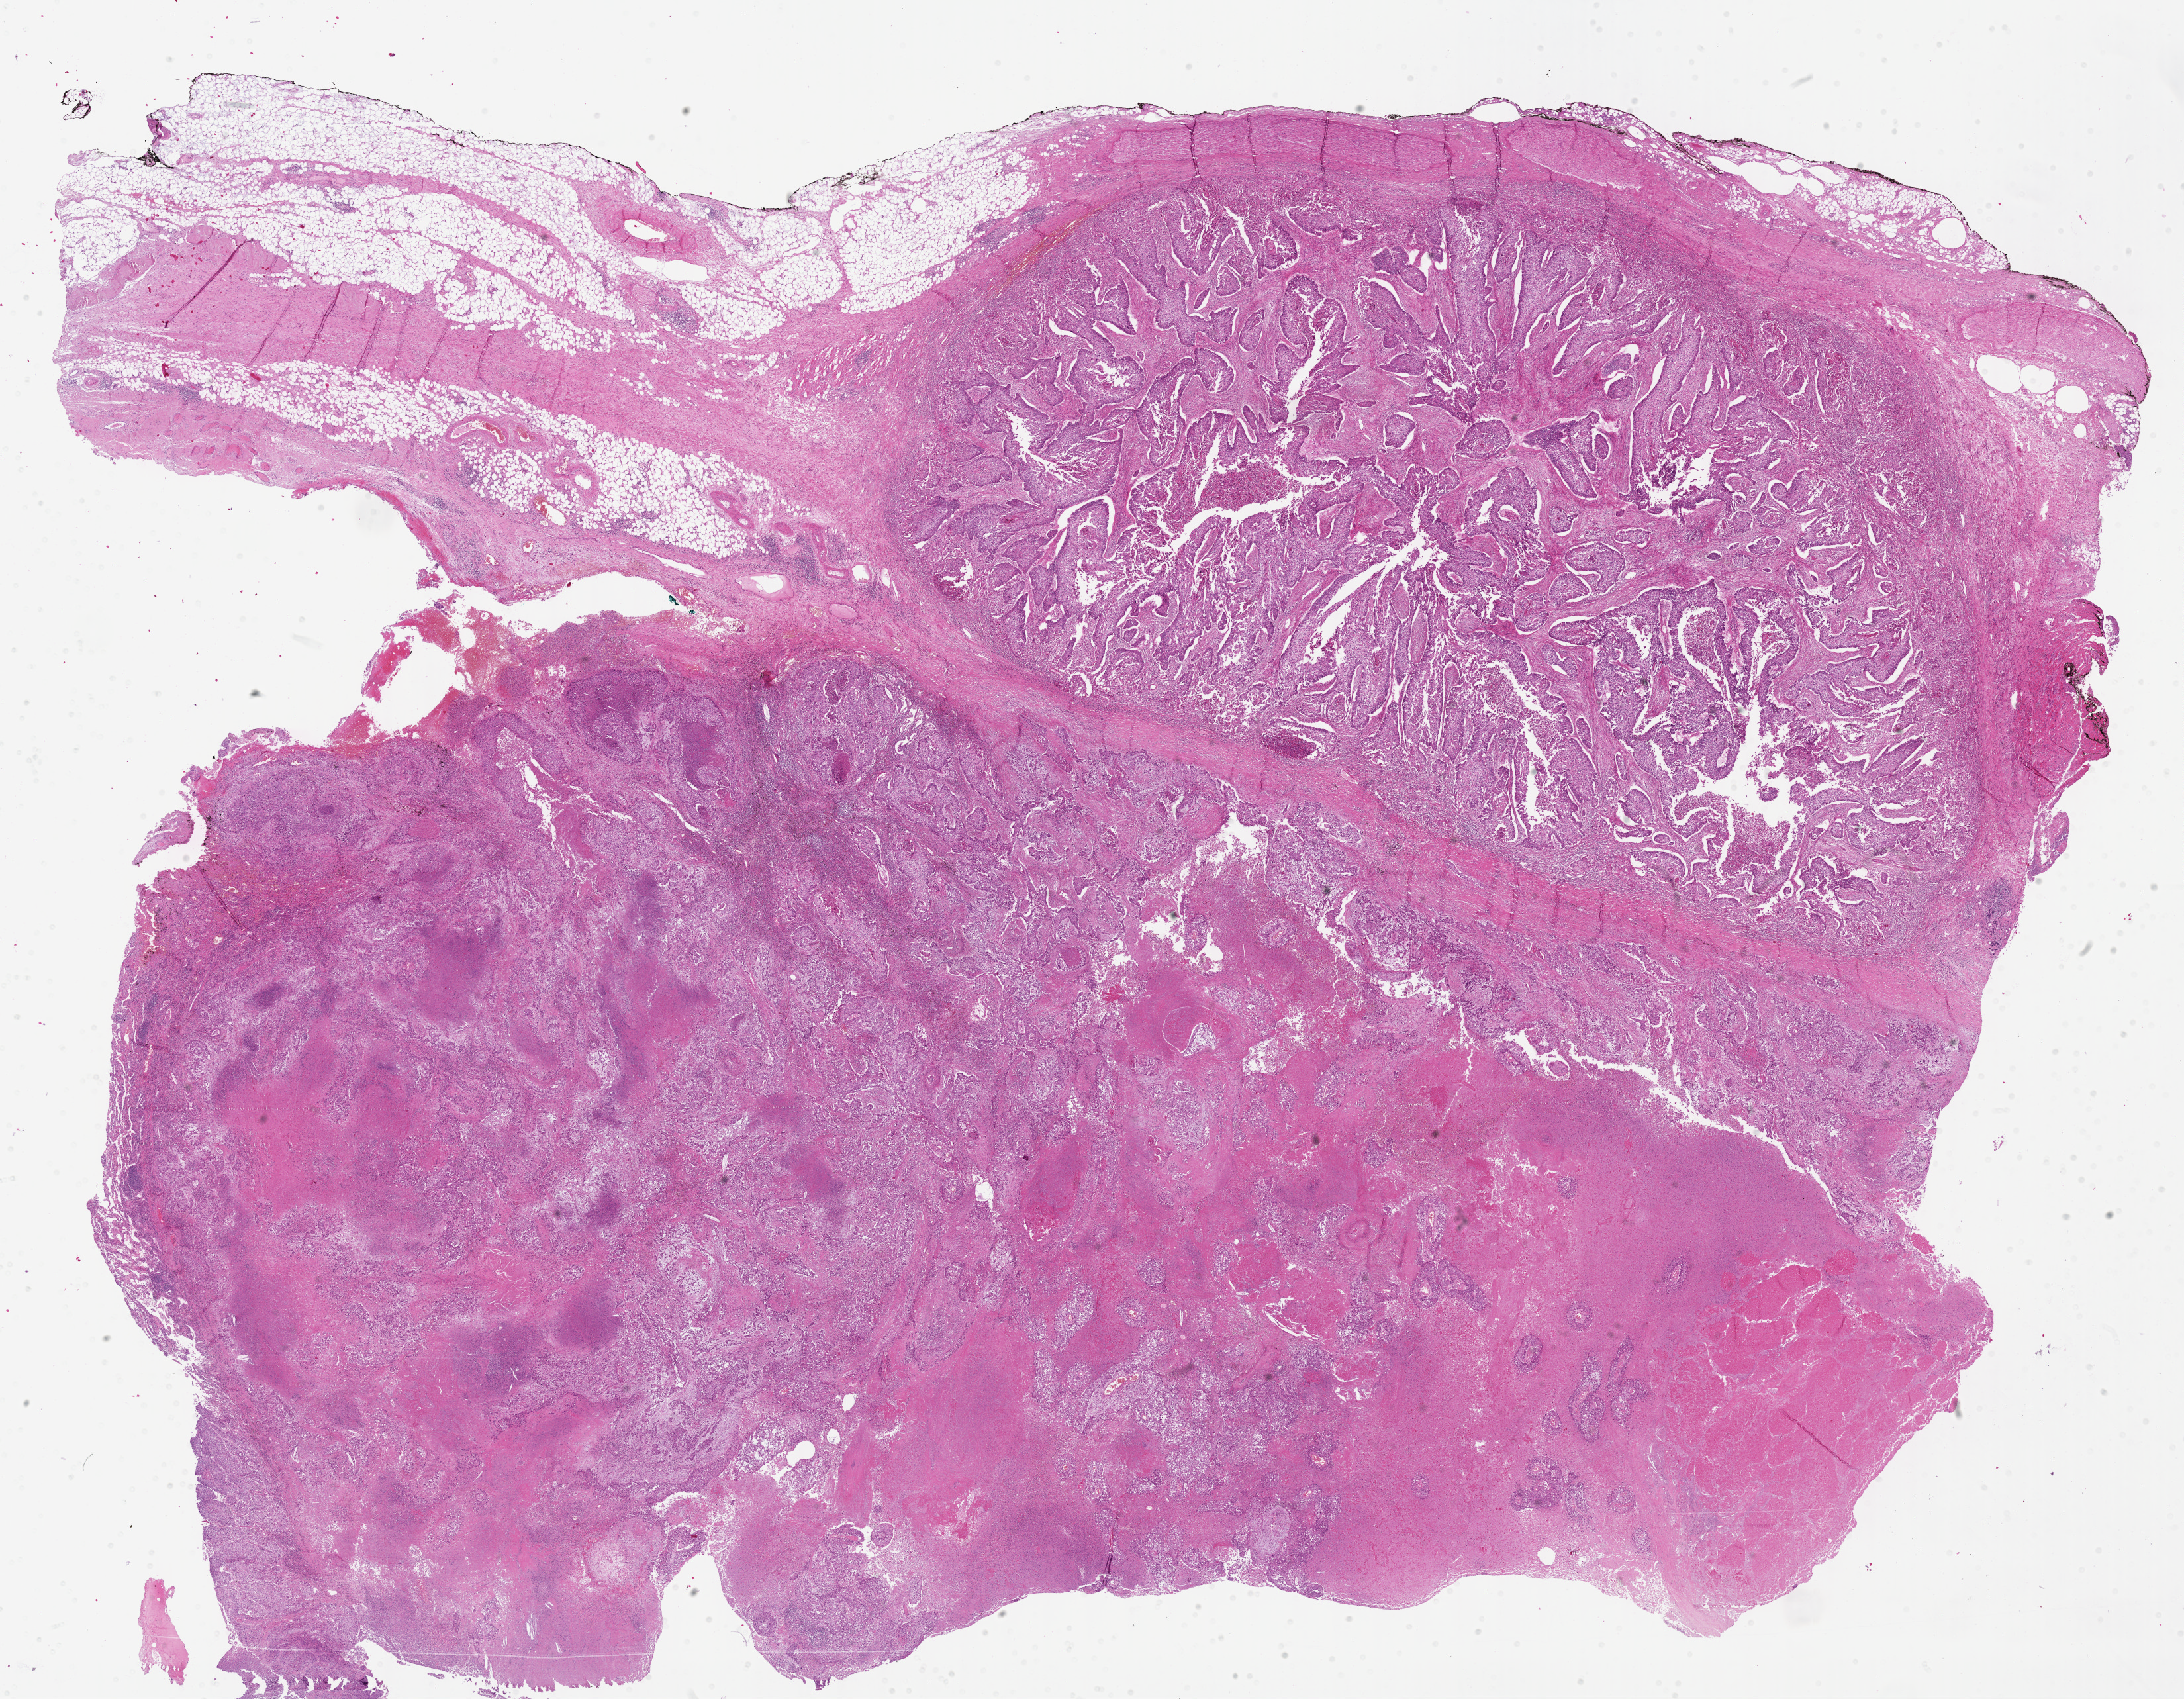
Digitized H&E-stained tissue section (whole slide), shown as a low-resolution overview of the whole scanned area (about 26.7 x 20.7 mm, acquisition: 40x scan), FFPE section, lung, primary tumour sample. Male patient; age at initial diagnosis 79 years.
Diagnosis: Squamous cell carcinoma, NOS (upper lobe, lung). Laterality: left. AJCC pathologic stage: IIB.